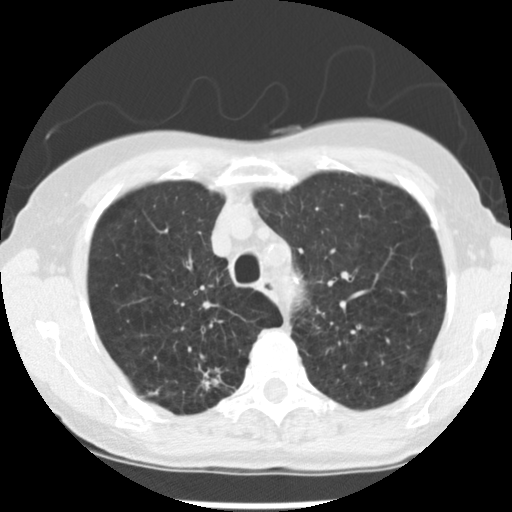
Axial slice from a low-dose chest CT screening exam. First (baseline) screen. Lung window (W 1500 / L -600 HU). 2.5 mm slice thickness. Standard (soft-tissue) reconstruction kernel (STANDARD). 120 kVp. Slice 56 of 265 in the series. Female, age 72 years at enrolment. Current smoker at enrolment.
Lesion marked by an expert reader, bounding box [x1, y1, x2, y2] px = [184, 353, 240, 406]. The screening reader recorded 3 non-calcified nodules or masses ≥4 mm on this exam (right upper lobe, left upper lobe, left lower lobe); which of them this box marks is not recorded. Lung cancer was diagnosed 50 days after this screen: adenocarcinoma, NOS, right upper lobe, moderately differentiated (G2), stage IB (AJCC 6th edition), 22 mm at pathology.